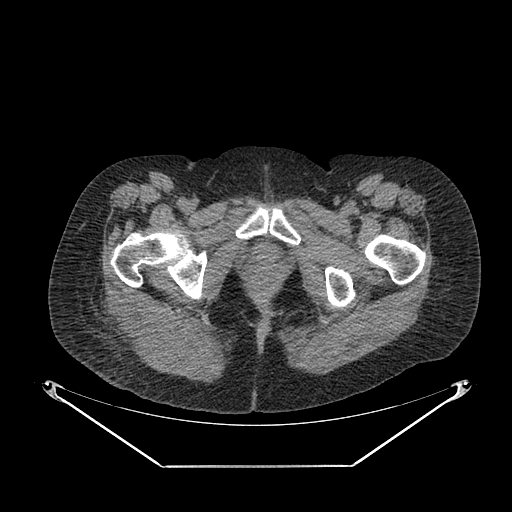
CT of an extremity soft-tissue mass (from a PET/CT study), one axial slice; position 46 of 267 along the scan axis; reconstruction kernel SOFT; 140 kVp; soft-tissue window (W 400 / L 40 HU); 512 × 512 image matrix, field of view 500 × 500 mm. Female patient. From the clinical record (not read from this slice): histological type: spindle cell suggestive of myxofibrosarcoma; grade: intermediate; site of the primary tumour: right buttock.
Structures marked on this image (expert contour drawn on MRI and transferred to this co-registered scan by the dataset authors):
- gross tumour volume (mass): box from (x=107, y=299) to (x=172, y=350) px